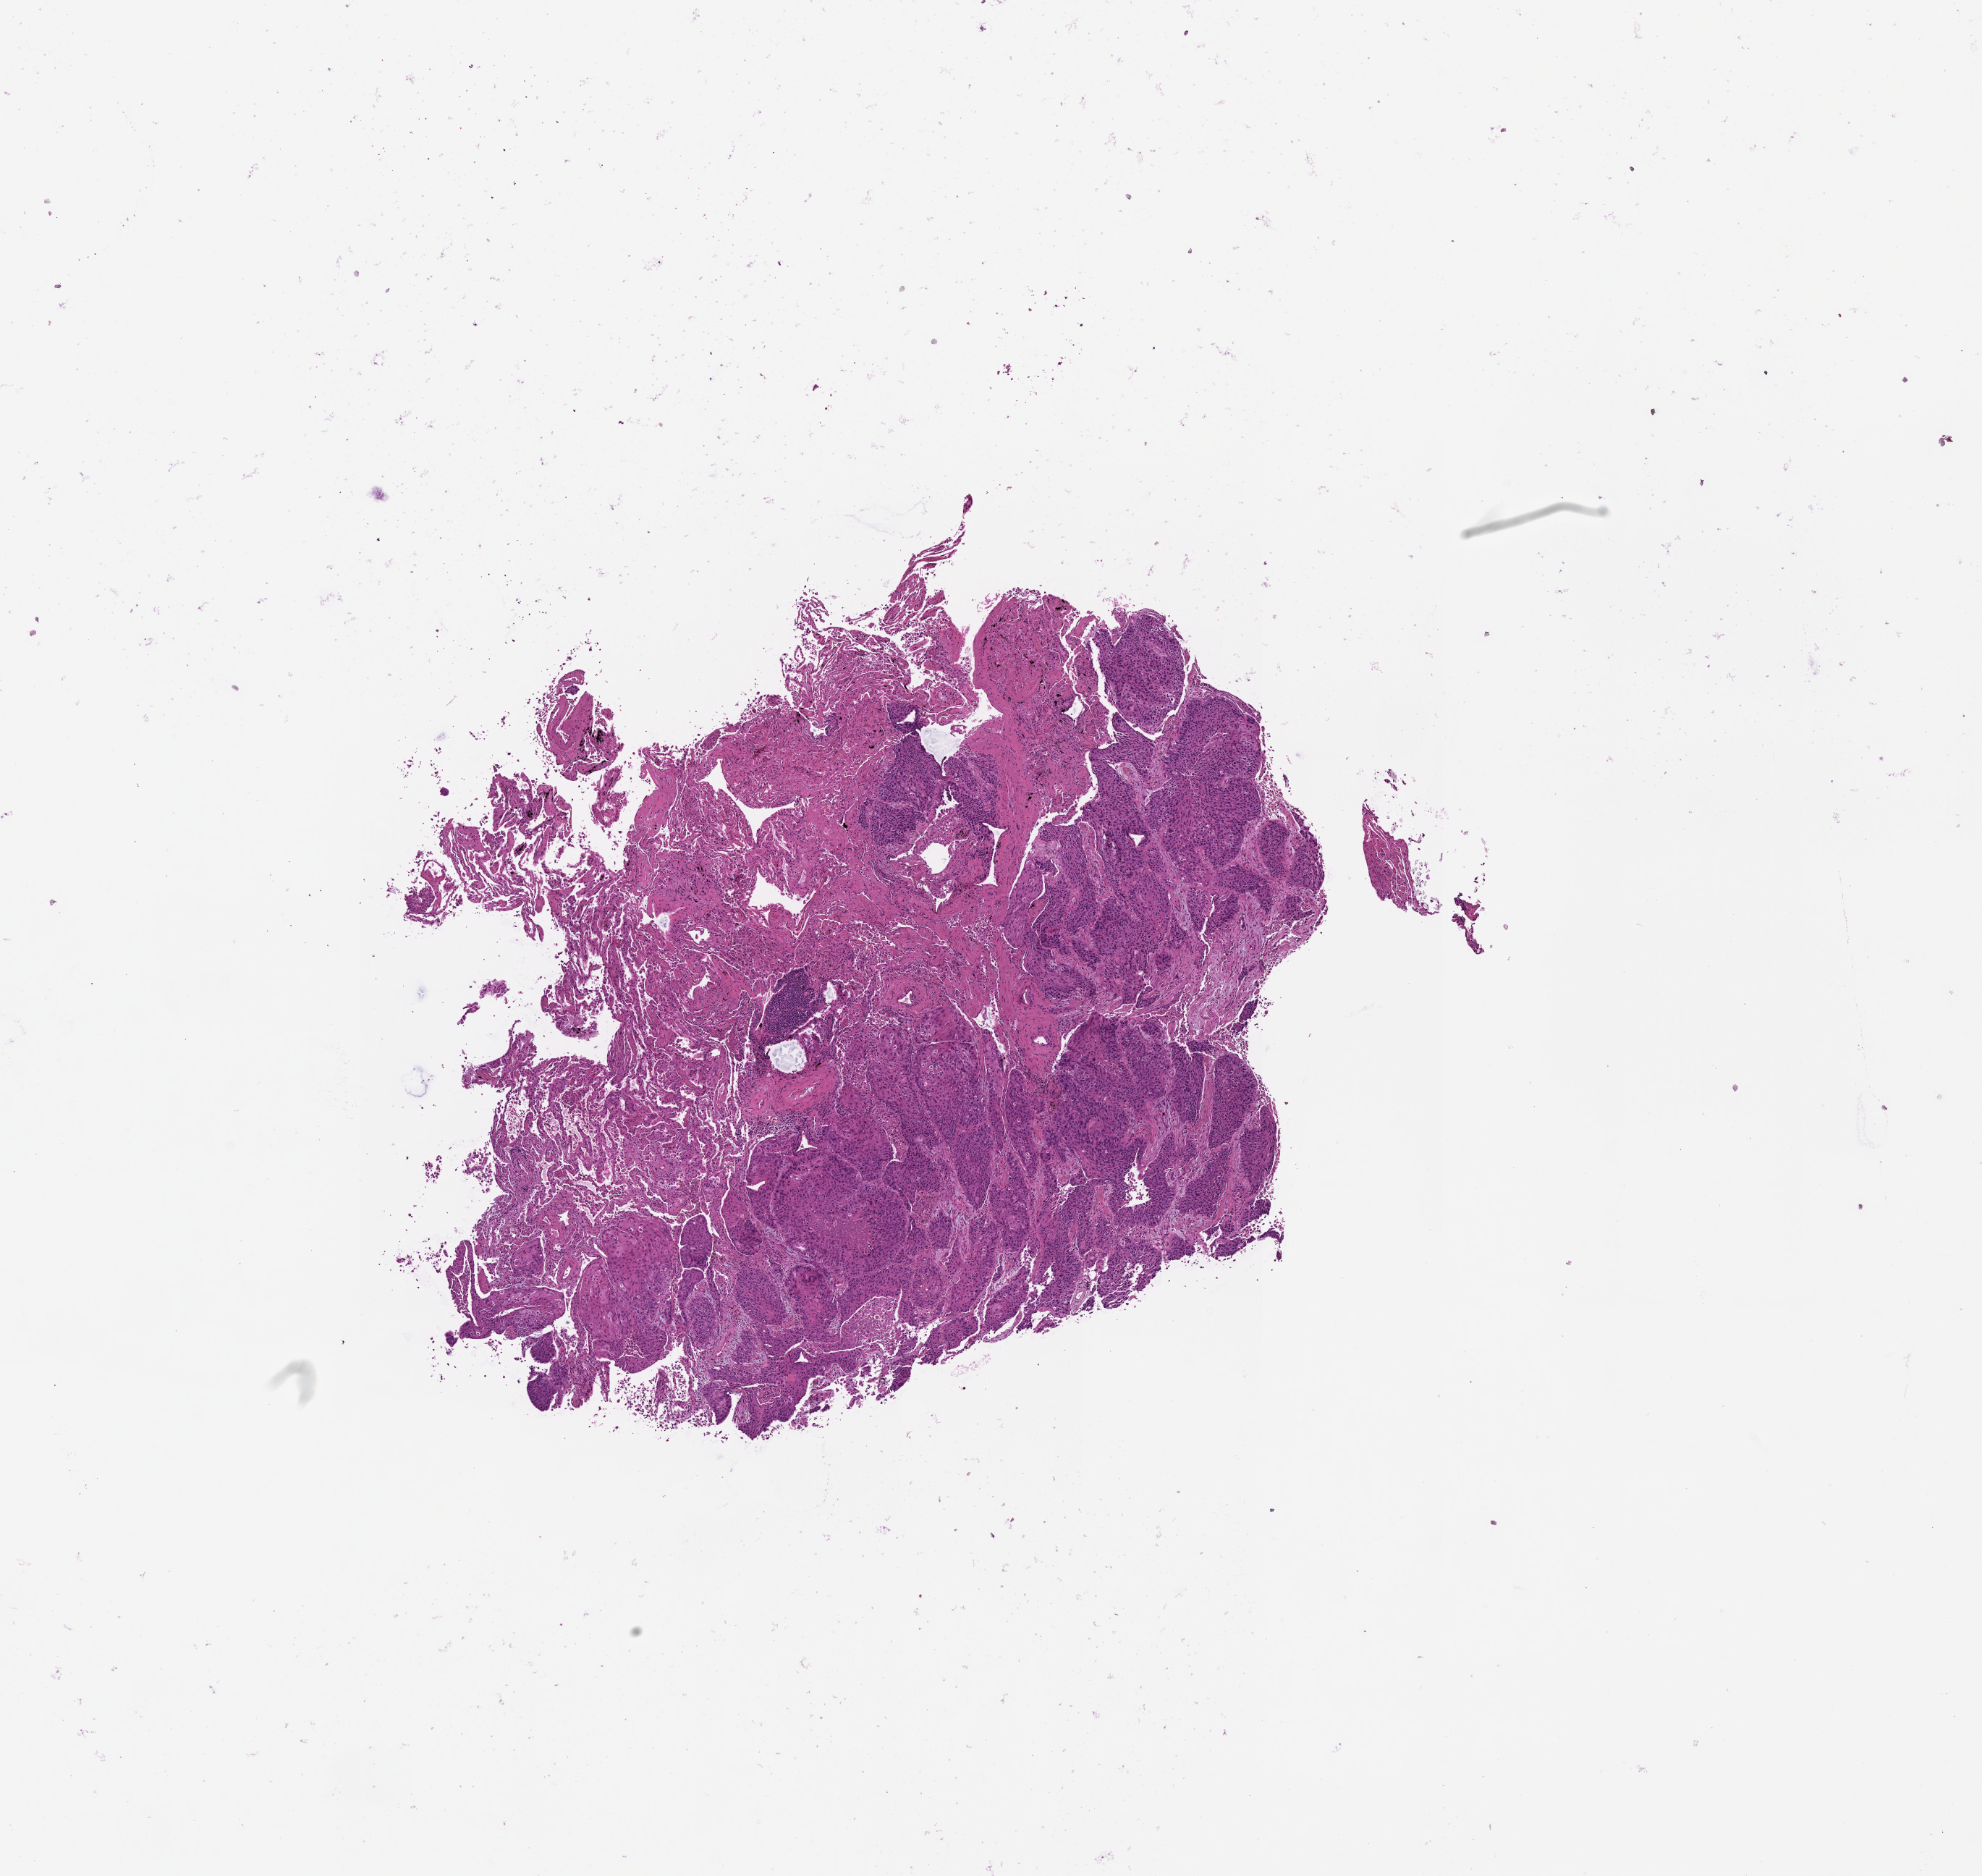
H&E-stained whole-slide image, shown as a low-resolution overview of the whole scanned area (about 11.0 x 10.4 mm, acquisition: 20x scan). Lung, tissue type not recorded.
Patient diagnosis (cohort enrolment): squamous cell carcinoma (lung).